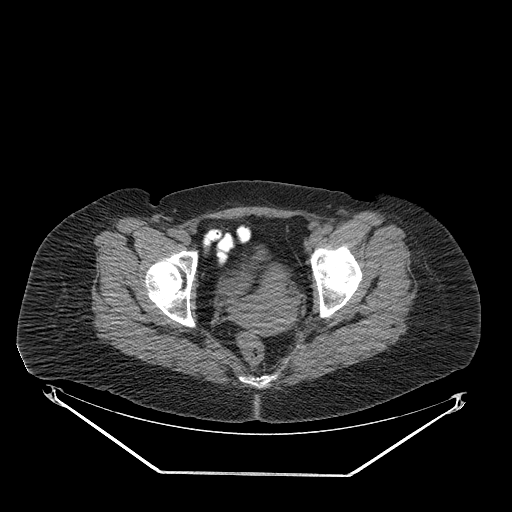
CT of an extremity soft-tissue mass (from a PET/CT study), one axial slice. Position 64 of 267 along the scan axis. Reconstruction kernel STANDARD. Soft-tissue window (W 400 / L 40 HU). 512 × 512 image matrix, field of view 500 × 500 mm. Female patient. Case-level facts recorded for this patient, not image findings: histological type: myxofibrosarcoma; grade: intermediate; site of the primary tumour: left thigh.
Outlined on this slice (expert contour drawn on MRI and transferred to this co-registered scan by the dataset authors):
- gross tumour volume including surrounding oedema: bounding box (x1, y1, x2, y2) in pixels: (311, 238, 321, 248)